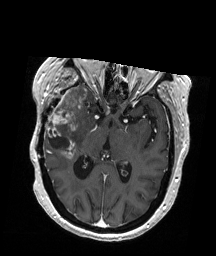
Brain MRI from a brain-tumour surgery series, one axial slice. Position 108 of 192 along the scan axis. T1-weighted post-contrast. 216 × 256 image matrix, field of view 211 × 250 mm. Case-level facts recorded for this patient, not image findings: histopathology: Glioblastoma; WHO grade: 4; IDH mutation: no.
Annotated regions visible in this slice (expert manual segmentation):
- tumour: bounding box (x1, y1, x2, y2) in pixels: (45, 86, 87, 159)